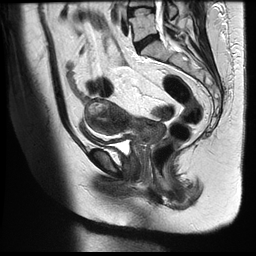
Pelvic MRI for cervical cancer, one sagittal slice. Position 18 of 35 along the scan axis. T2-weighted. 1.5 T. TE 122.8 ms, TR 4992 ms. 256 × 256 image matrix. Female patient, age 42 years.
Structures marked on this image (expert manual segmentation):
- uterus and cervix: bounding box [x1, y1, x2, y2] px = [83, 97, 166, 155]